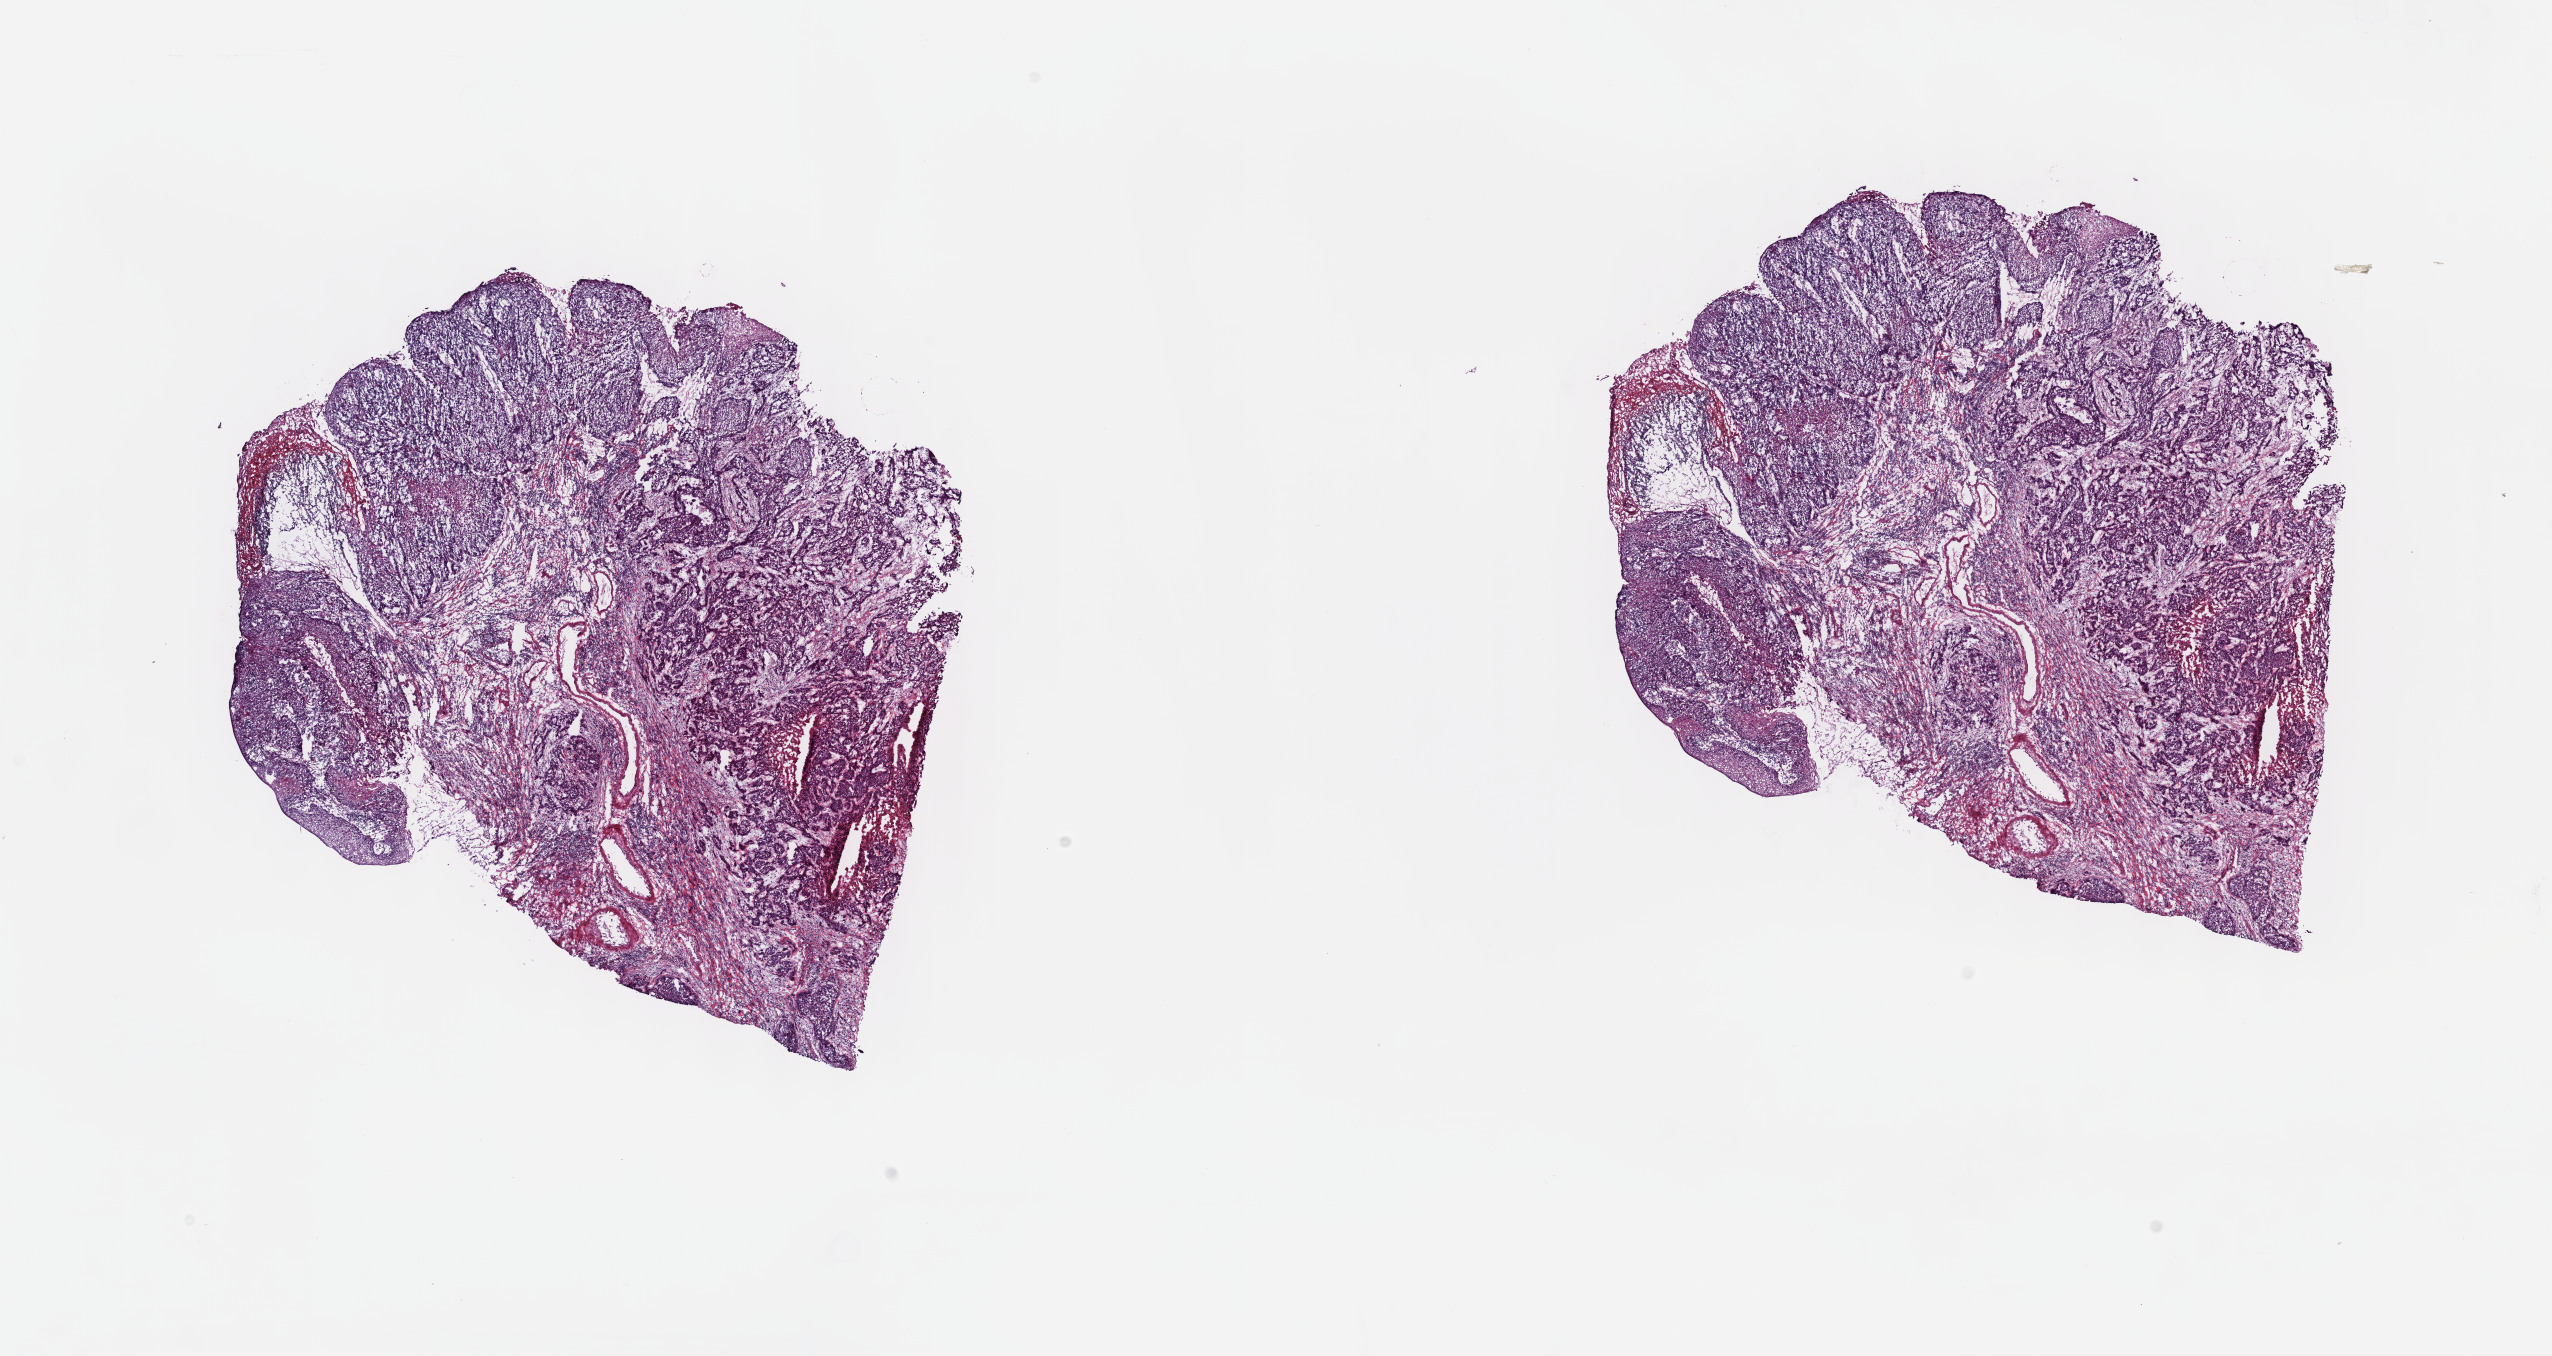
H&E whole-slide image — whole scanned area (about 20.6 x 11.0 mm, slide scanned at 40x) shown as a low-resolution overview. Frozen section from the top of the tissue portion. Esophagus, primary tumour sample. Patient: male, age at initial diagnosis 56 years. Histologic grade: G3 (poorly differentiated). Composition of this section per pathologist review: tumour cells 58%, tumour nuclei 70%, normal cells 0%, stromal cells 35%, necrosis 7%. Infiltration values recorded for this section: lymphocyte infiltration 22%, monocyte infiltration 0%, neutrophil infiltration 3%.
AJCC pathologic stage: IIA (6th edition). Histologic diagnosis: Squamous cell carcinoma, NOS (middle third of esophagus).